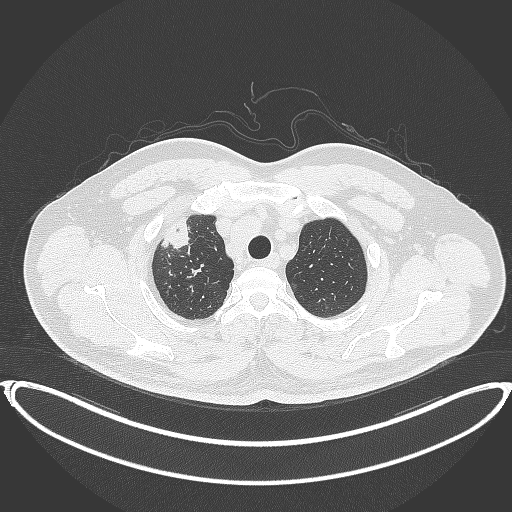
Chest CT, one axial slice. Position 336 of 399 along the scan axis. Reconstruction kernel B70f. 120 kVp. Lung window (W 1500 / L -600 HU). 1 mm slice thickness. 512 × 512 image matrix, field of view 445 × 445 mm. Male patient, age 53 years. From the clinical record (not read from this slice): clinical TNM (as recorded): T2a N0 M0.
Outlined on this slice (rectangle marked by the reading radiologist):
- lung tumour (recorded histology: adenocarcinoma): bounding box [x1, y1, x2, y2] px = [160, 213, 194, 251]